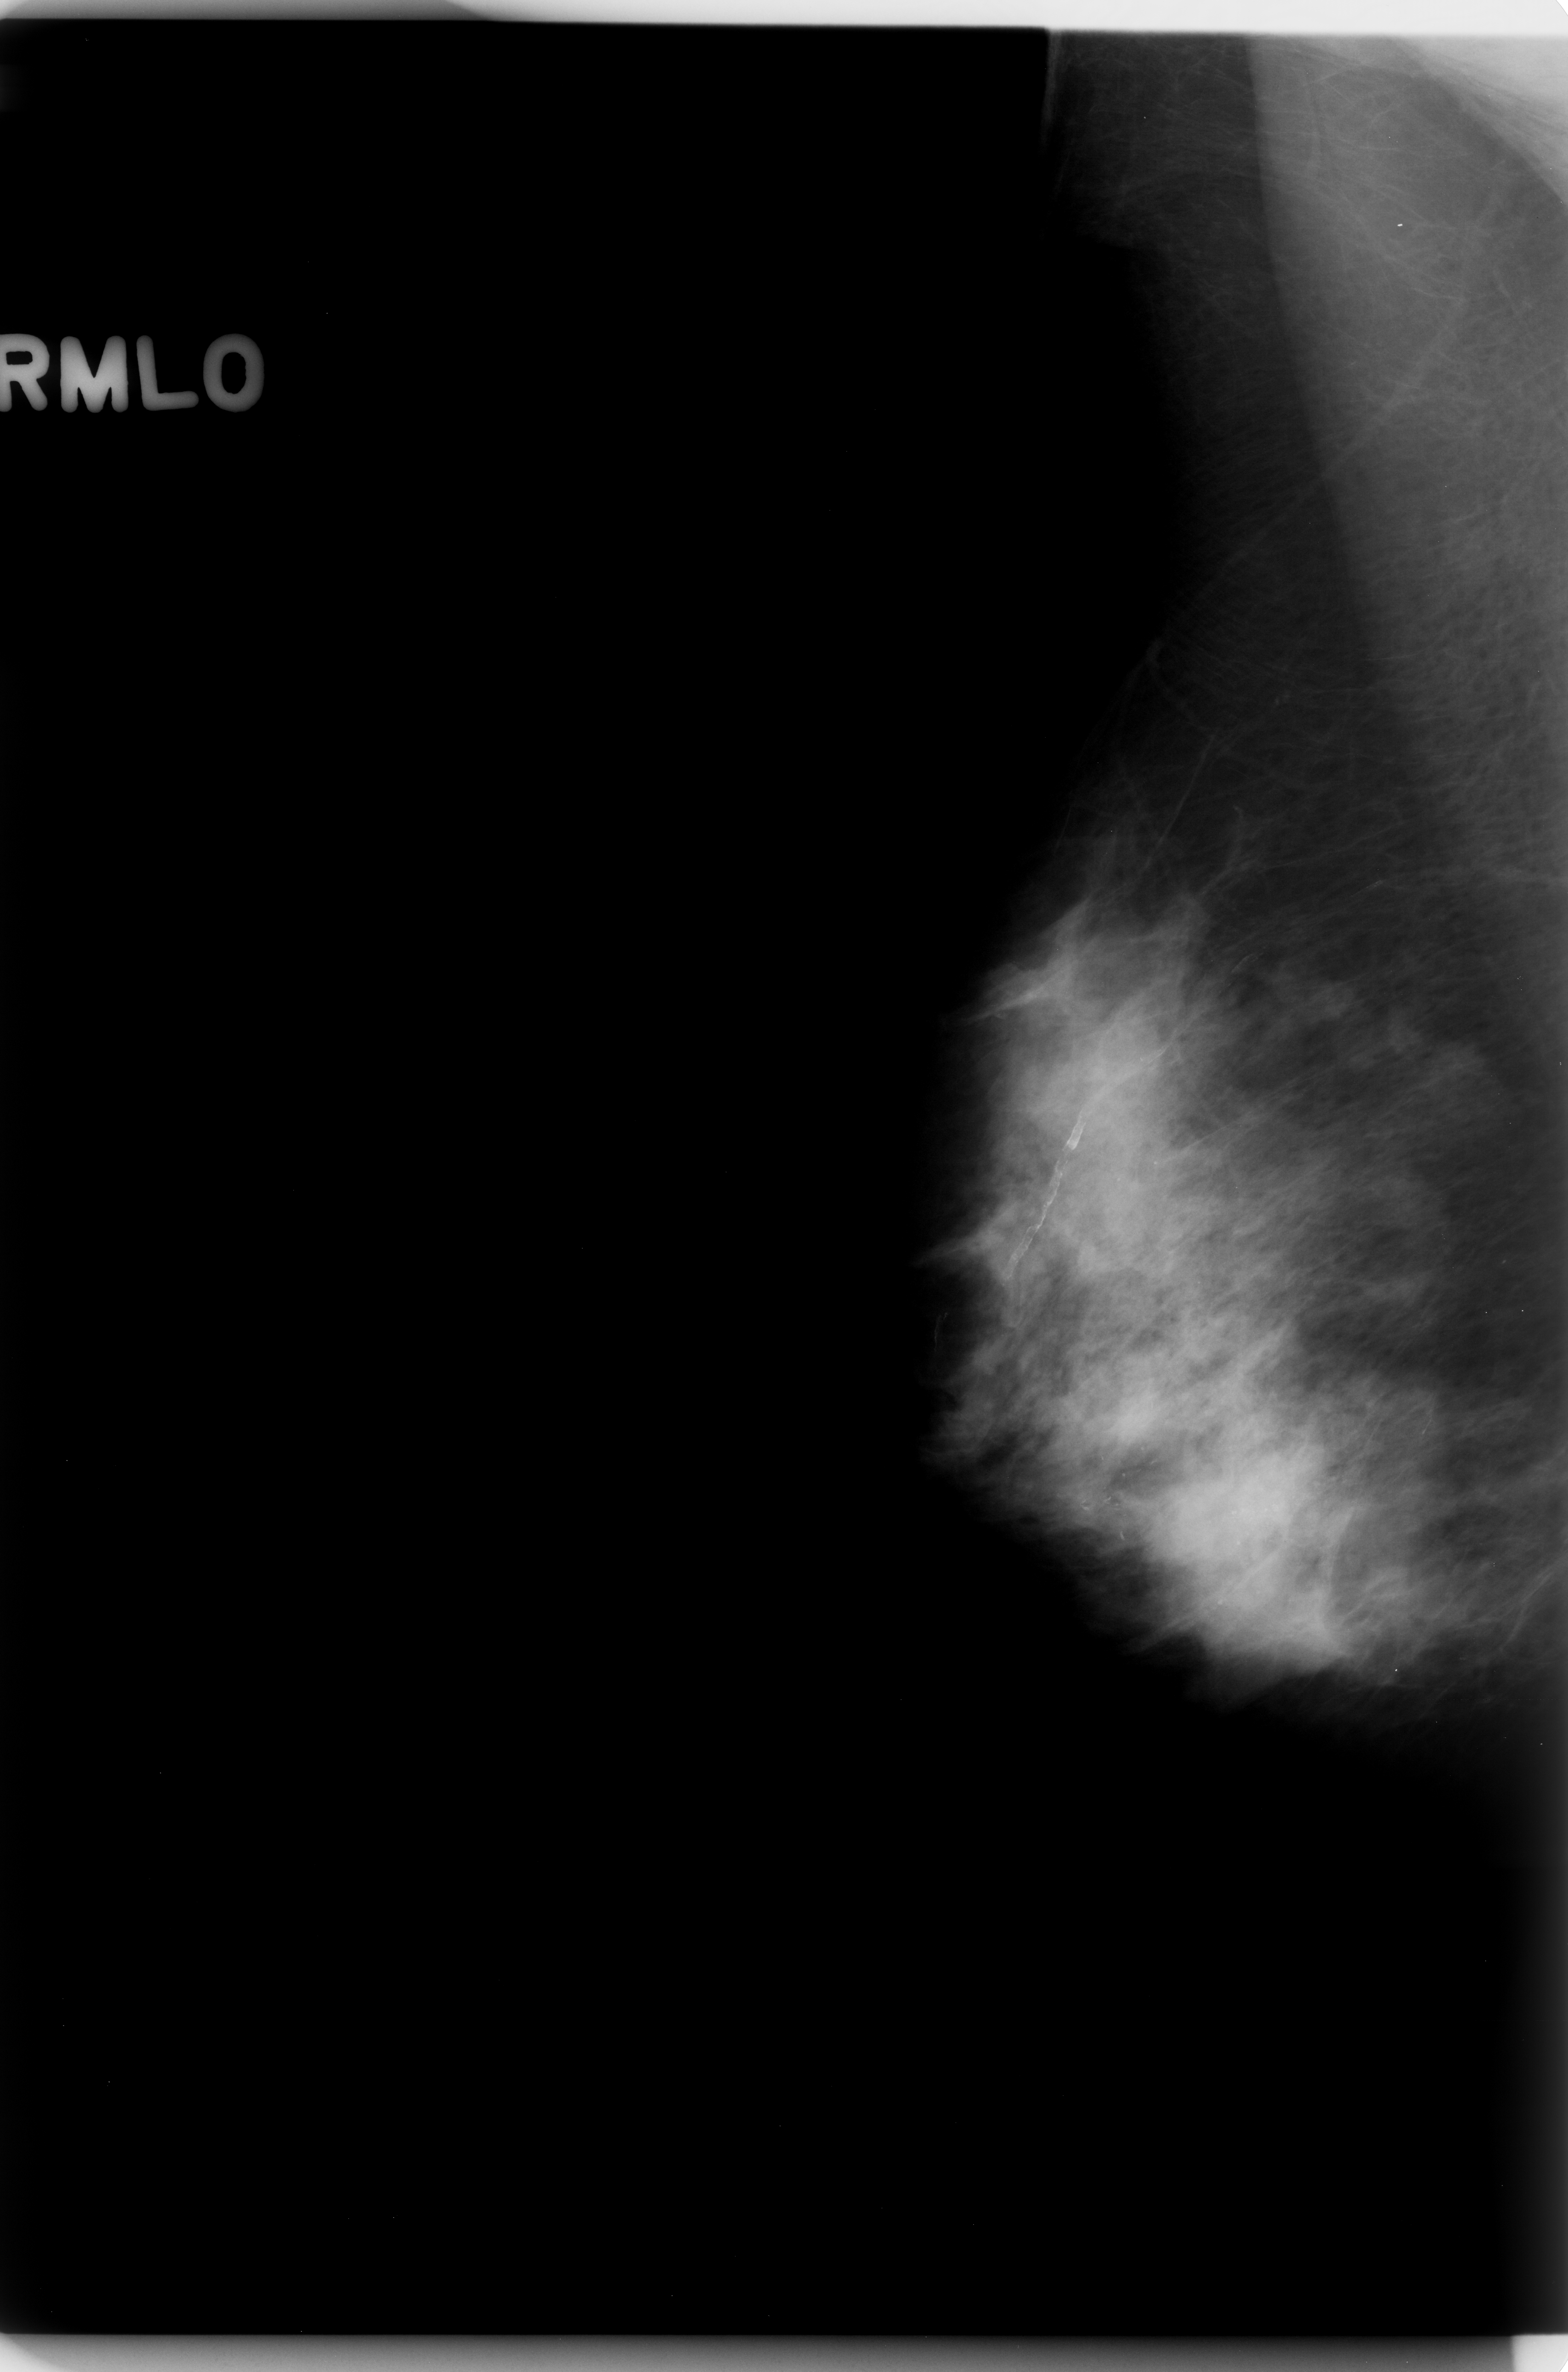
Scanned film-screen mammogram; right breast; mediolateral oblique (MLO) view; BI-RADS breast density category 3 (scale 1–4).
Marked findings (only marked abnormalities are described; nothing is implied about the rest of the image): calcifications, morphology fine linear branching, distribution segmental; BI-RADS assessment category 5; subtlety rating 4 on a 1 (subtle) to 5 (obvious) scale; pathology (as recorded): malignant.